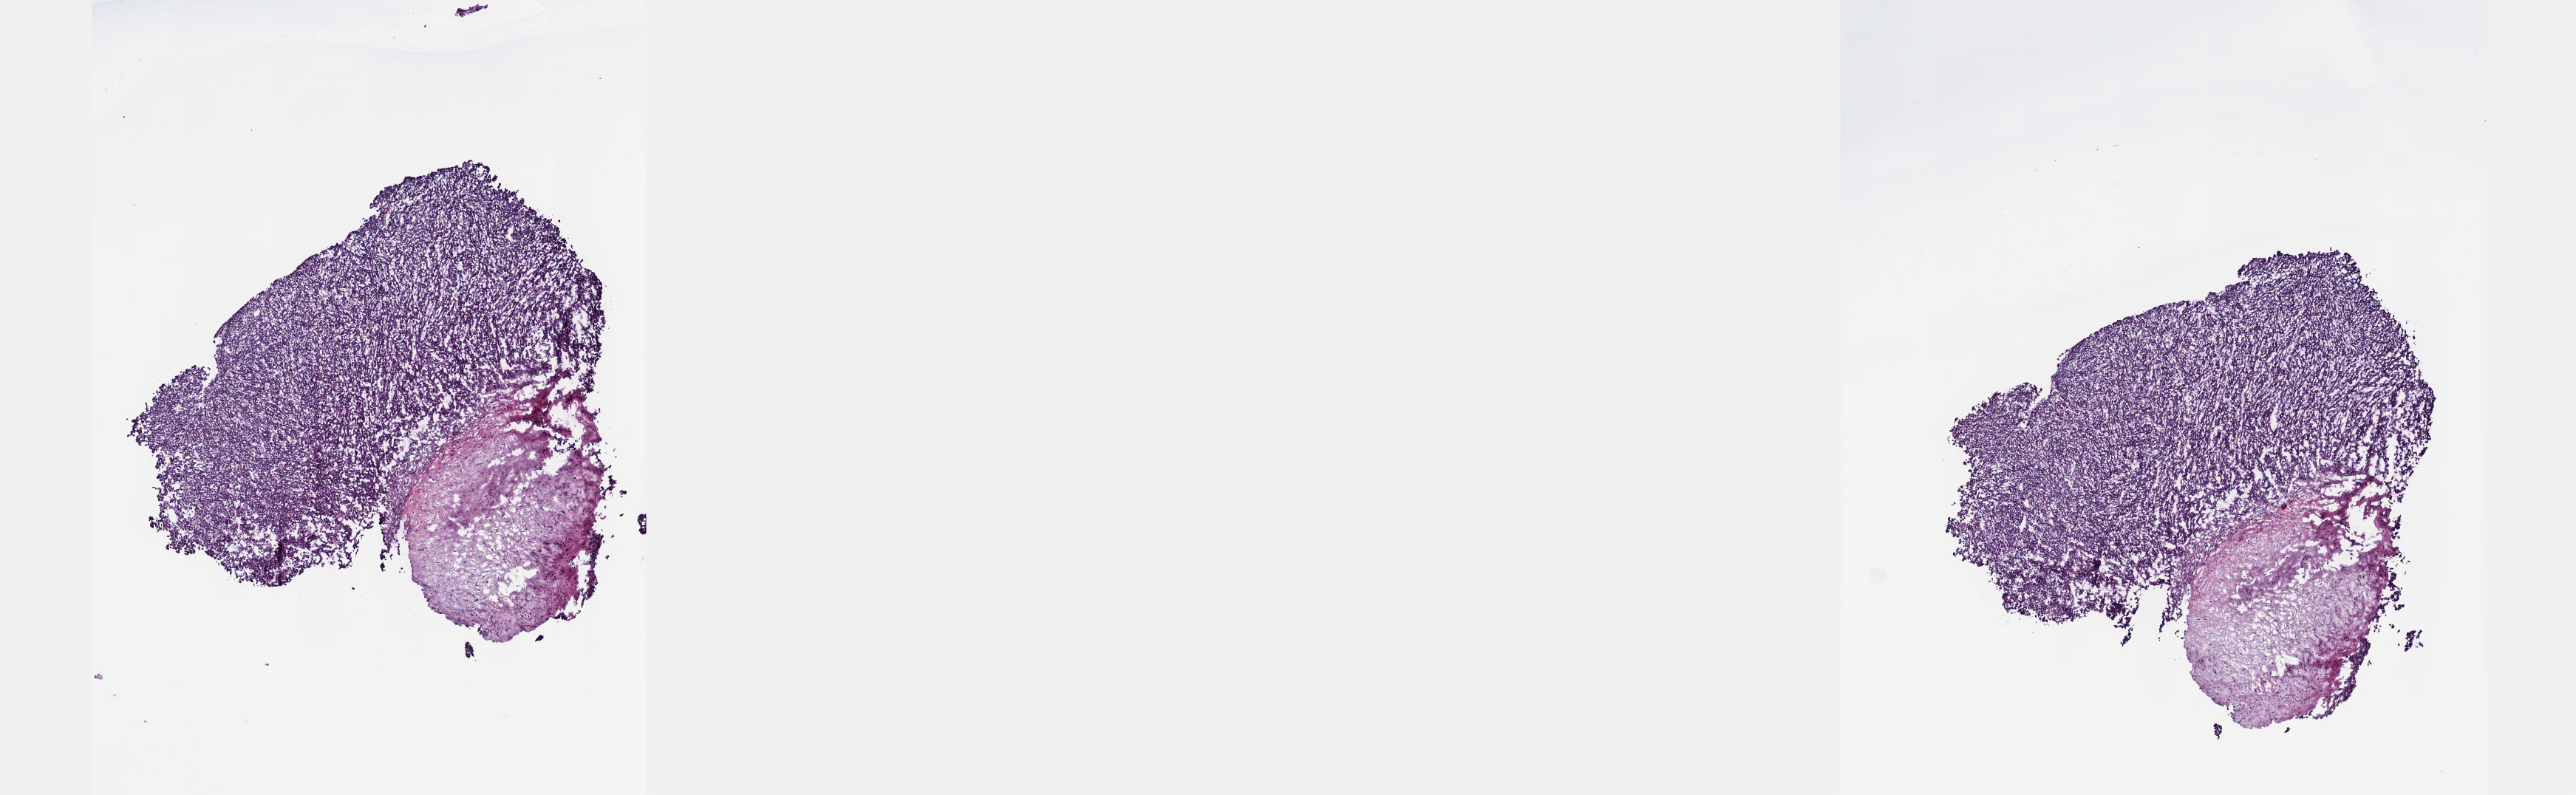
H&E whole-slide image — low-resolution overview of the scanned area, about 14.1 x 4.3 mm (acquisition: 40x scan), frozen section from the top of the tissue portion, sample: primary tumour, liver. Male, age 64 years at initial diagnosis. Histologic grade: G2 (moderately differentiated). Pathologist review of this section (percent, as recorded): tumour cells 65%, tumour nuclei 75%, normal cells 35%, stromal cells 0%, necrosis 0%. Inflammatory infiltration, as recorded: lymphocyte infiltration 2%, monocyte infiltration 0%, neutrophil infiltration 0%.
Diagnosis: Hepatocellular carcinoma, NOS. AJCC pathologic stage: II.